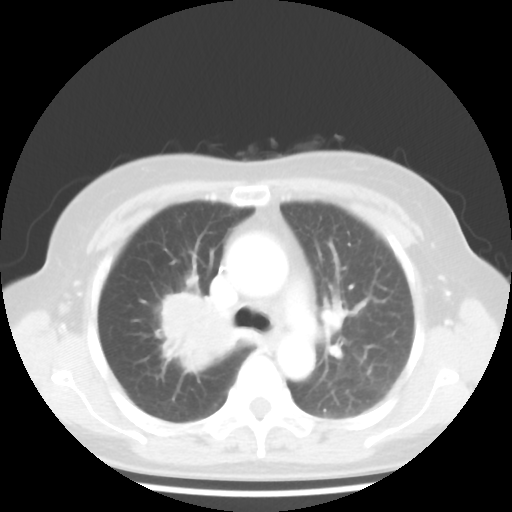
Chest CT, one axial slice; slice 29 of 44 in the series (ordered by position); reconstruction kernel STANDARD; 100 kVp; lung window (W 1500 / L -600 HU); 5 mm slice thickness; 512 × 512 image matrix, field of view 316 × 316 mm. Patient: female, 62 years. From the clinical record (not read from this slice): clinical TNM (as recorded): T3 N0 M0.
Structures marked on this image (bounding box drawn by a radiologist):
- lung tumour (recorded histology: small cell carcinoma): bounding box (x1, y1, x2, y2) in pixels: (145, 284, 248, 380)